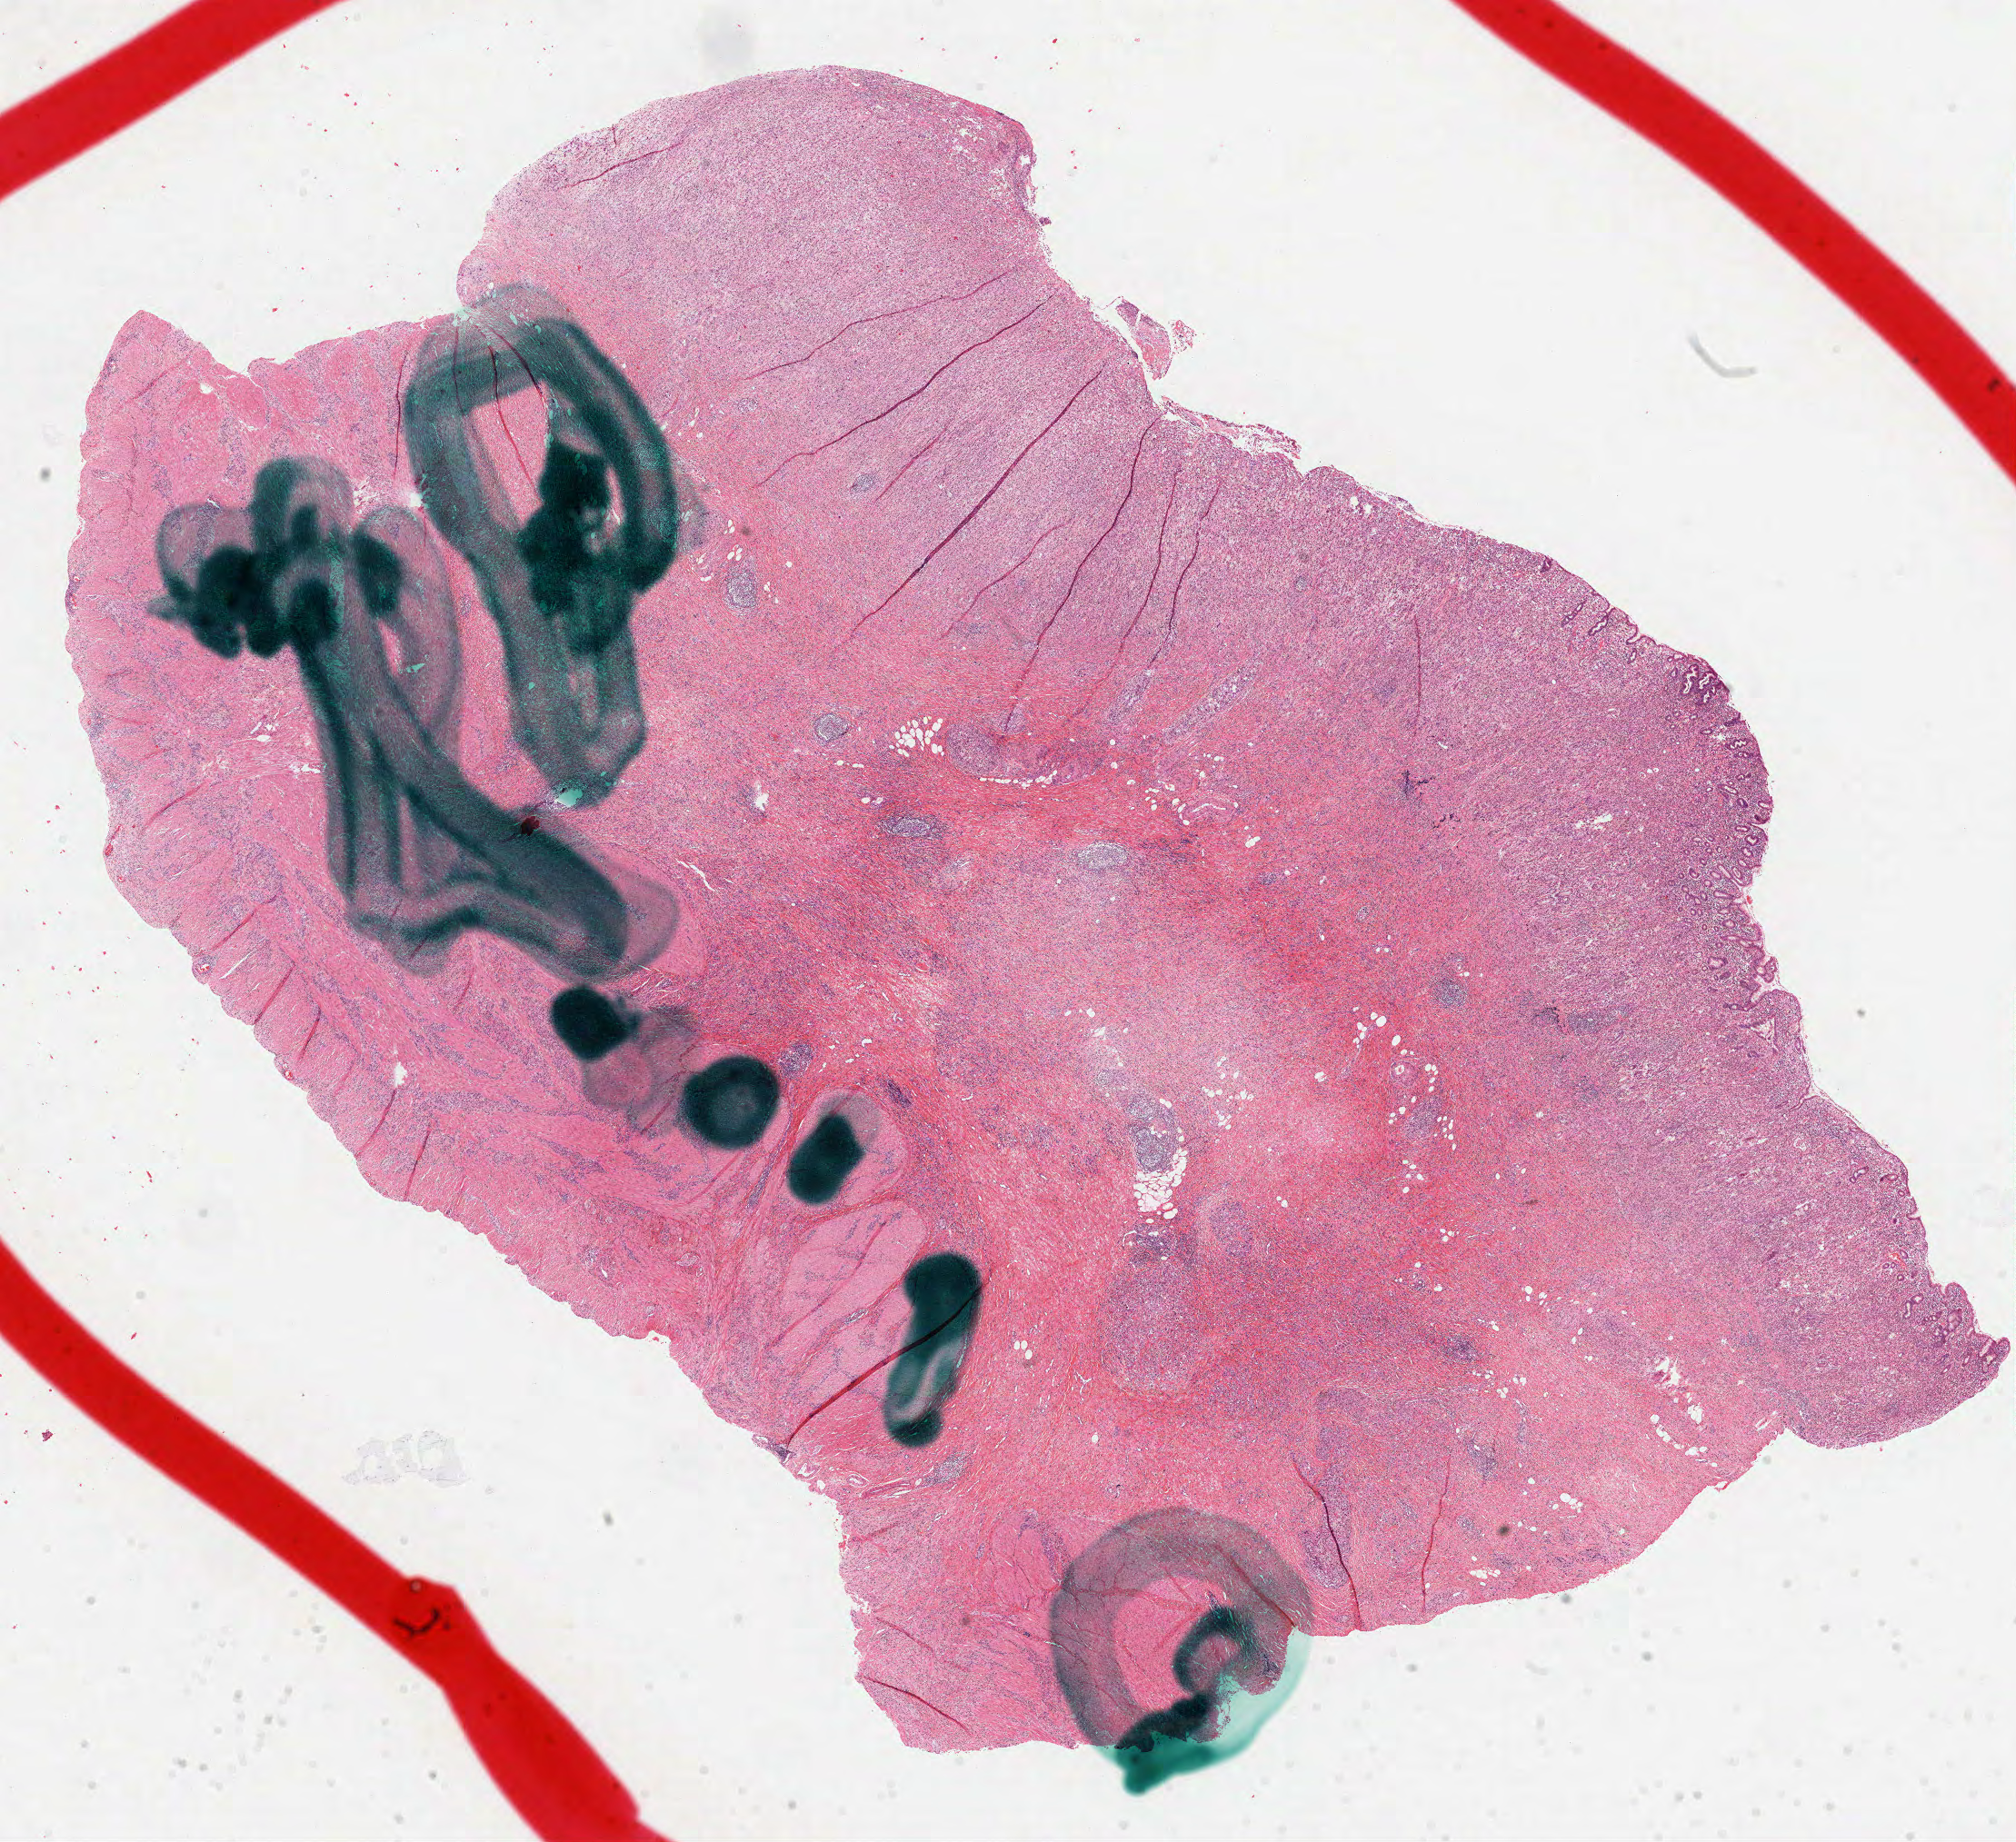
Whole-slide histology image, Hematoxylin and eosin (H&E) stained — a low-resolution overview of the entire scanned area, about 17.9 x 16.3 mm (slide scanned at 40x). Formalin-fixed paraffin-embedded (FFPE) diagnostic section. Sample: primary tumour, stomach. Patient: female, age at initial diagnosis 54 years. Histologic grade: G3 (poorly differentiated).
AJCC pathologic stage: IIA (7th edition). Lymph nodes positive (case pathology): 0 of 5 examined. Pathologic diagnosis: Carcinoma, diffuse type. TNM: T3 N0 M0.